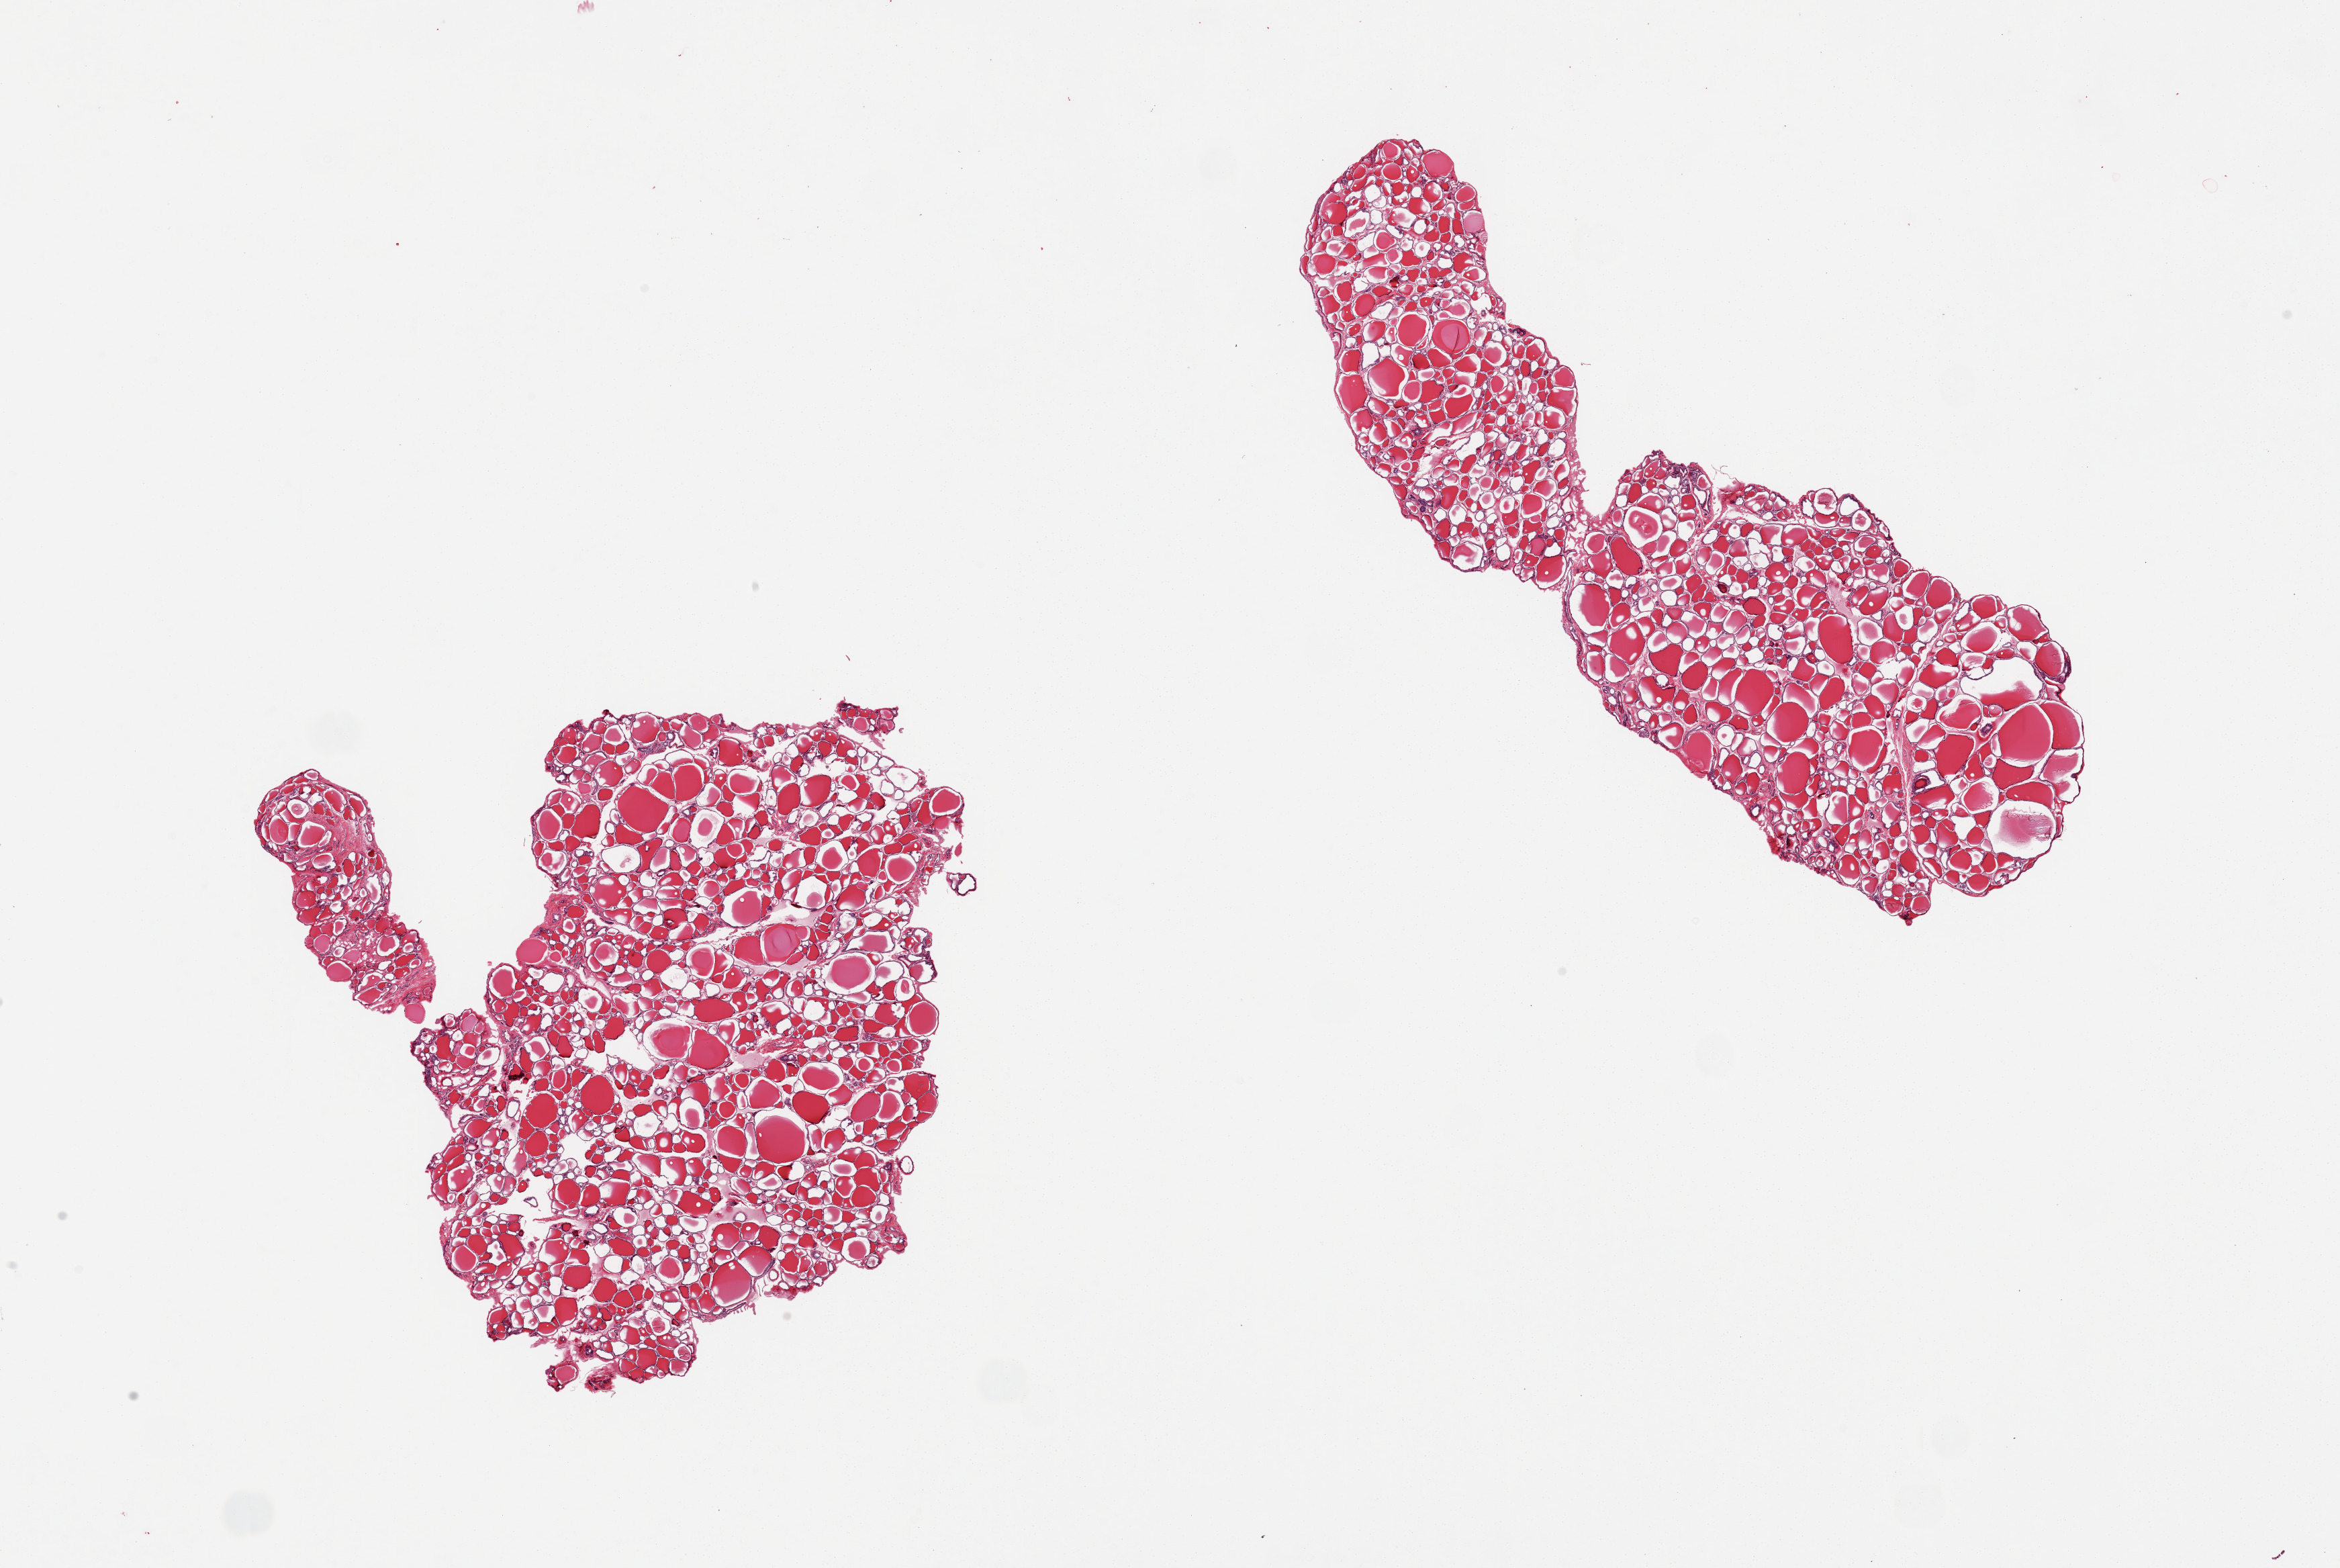
Whole-slide image, haematoxylin and eosin stain, brightfield, a low-resolution overview of the entire scanned area, about 27.6 x 18.5 mm. PAXgene-fixed, paraffin-embedded tissue. Target tissue: thyroid. Donor tissue sample.
- reviewer comment on this tissue sample: 2 pieces, well-preserved